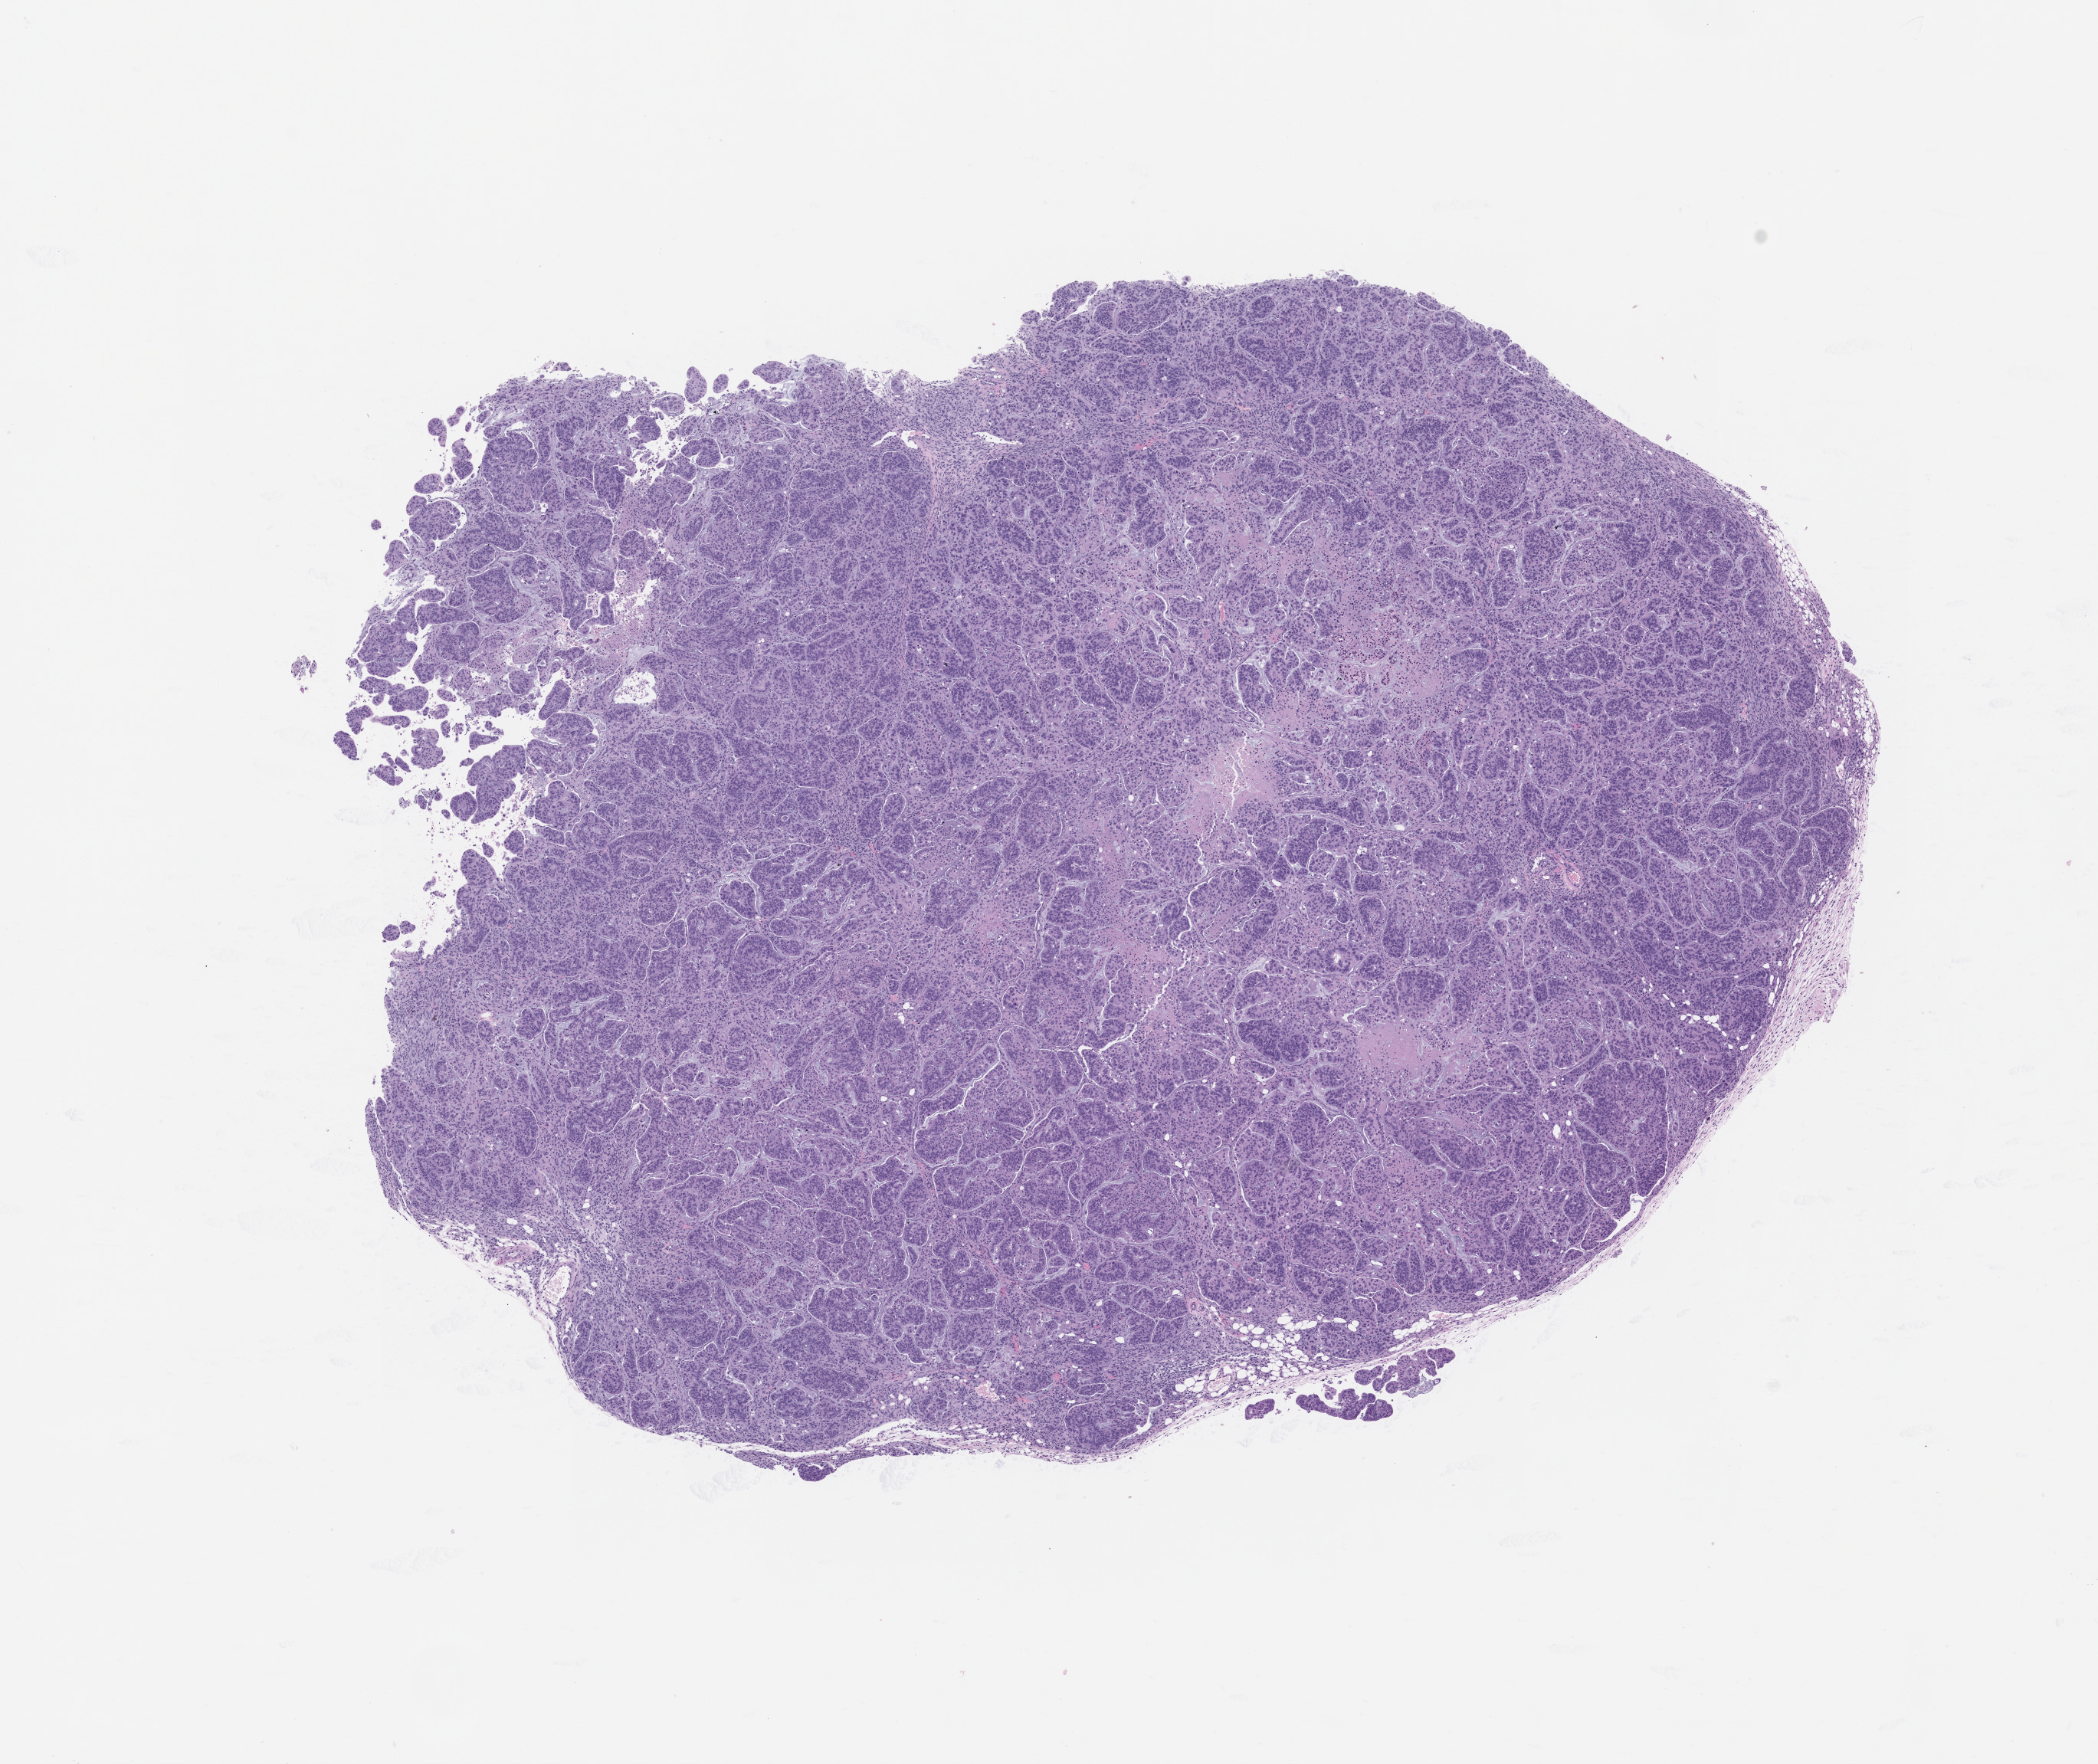
Whole-slide image, haematoxylin and eosin: patient-derived xenograft (human tumor grown in a mouse), passage 1, low-resolution overview of the scanned area, about 11.0 x 9.2 mm. FFPE section. Tumor site category: small intestine.
- originating patient diagnosis: Small Intestinal Adenocarcinoma